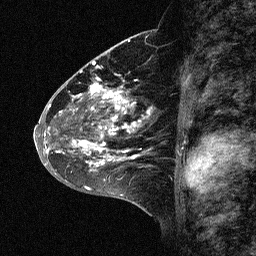
Breast MRI (dynamic contrast-enhanced), one sagittal slice; position 31 of 64 along the scan axis; dynamic contrast-enhanced study with each time point stored as its own series, time point 2 of 3 at this slice position (early post-contrast, ordered by acquisition time); 1.5 T; TE 4.5 ms, TR 11 ms; 256 × 256 image matrix, field of view 200 × 200 mm. Female patient, age 46 years. From the clinical record (not read from this slice): setting: breast cancer imaged before/during neoadjuvant chemotherapy; receptor status: HER2-positive.
Structures marked on this image (semi-automatic segmentation, software-assisted and operator-edited):
- analysis volume of interest (the breast-tissue region the enhancement analysis was run in; not a lesion): bounding box <43,72,170,177> (left, top, right, bottom; pixels)
- tumour enhancement mask (voxels above the 90 % enhancement threshold inside the analysis volume of interest): <44,74,149,171>